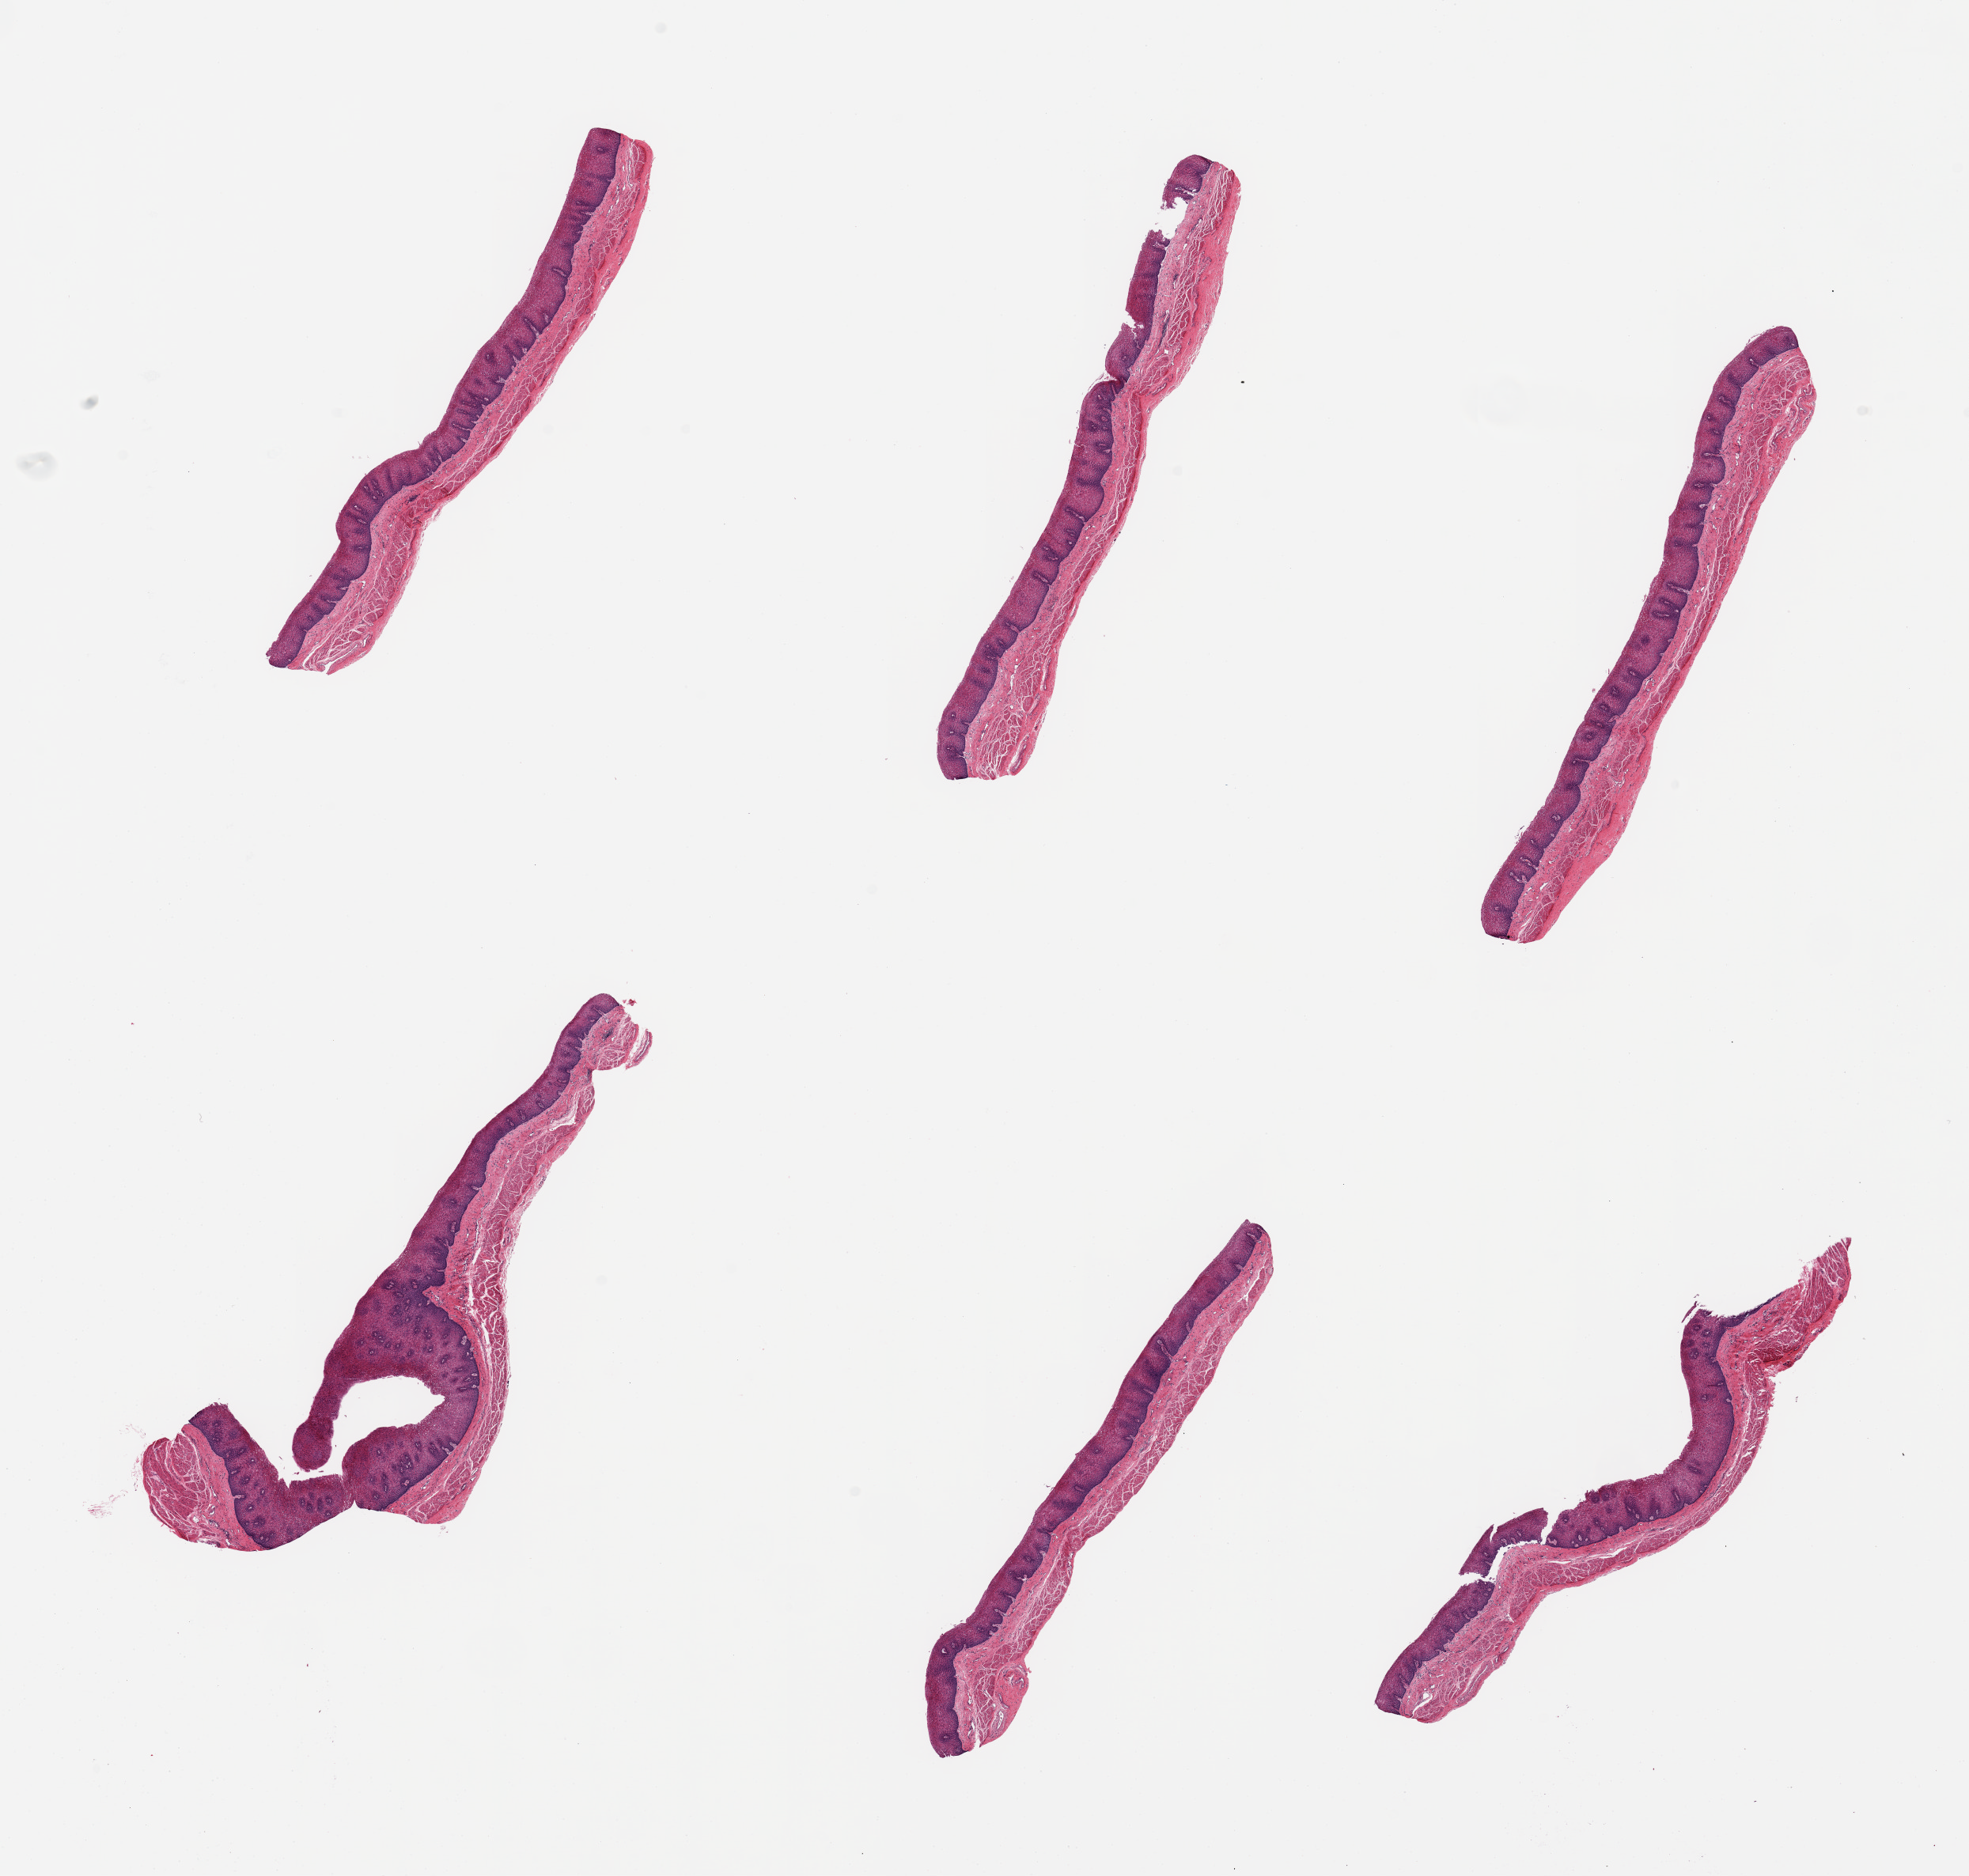
H&E whole-slide image, low-resolution overview of the scanned area, about 19.7 x 18.8 mm (acquisition: 20x scan). PAXgene-fixed, paraffin-embedded tissue. Section of esophageal mucous membrane (target tissue). Tissue donor sample. Donor: female.
- reviewer comment on this tissue sample: 6 pieces; well dissected